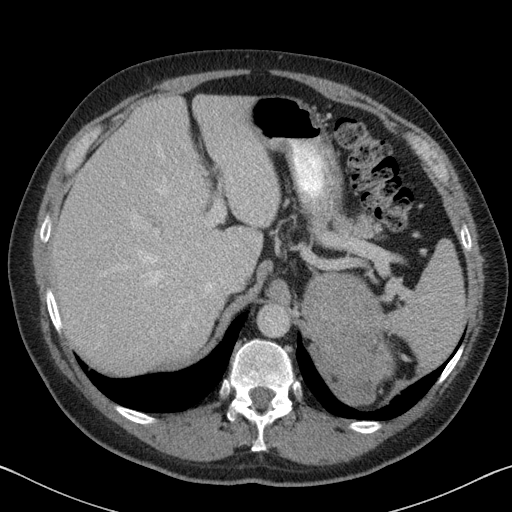
Contrast-enhanced abdominal CT, one axial slice. Position 61 of 88 along the scan axis. 120 kVp. Intravenous contrast given. Soft-tissue window (W 400 / L 40 HU). 512 × 512 image matrix, field of view 366 × 366 mm. Patient: male, 51 years. From the clinical record (not read from this slice): diagnosis: adrenocortical carcinoma; tumour side: left adrenal.
Outlined on this slice (semi-automatically segmented with operator editing):
- mass: bounding box <305,274,393,399> (left, top, right, bottom; pixels)